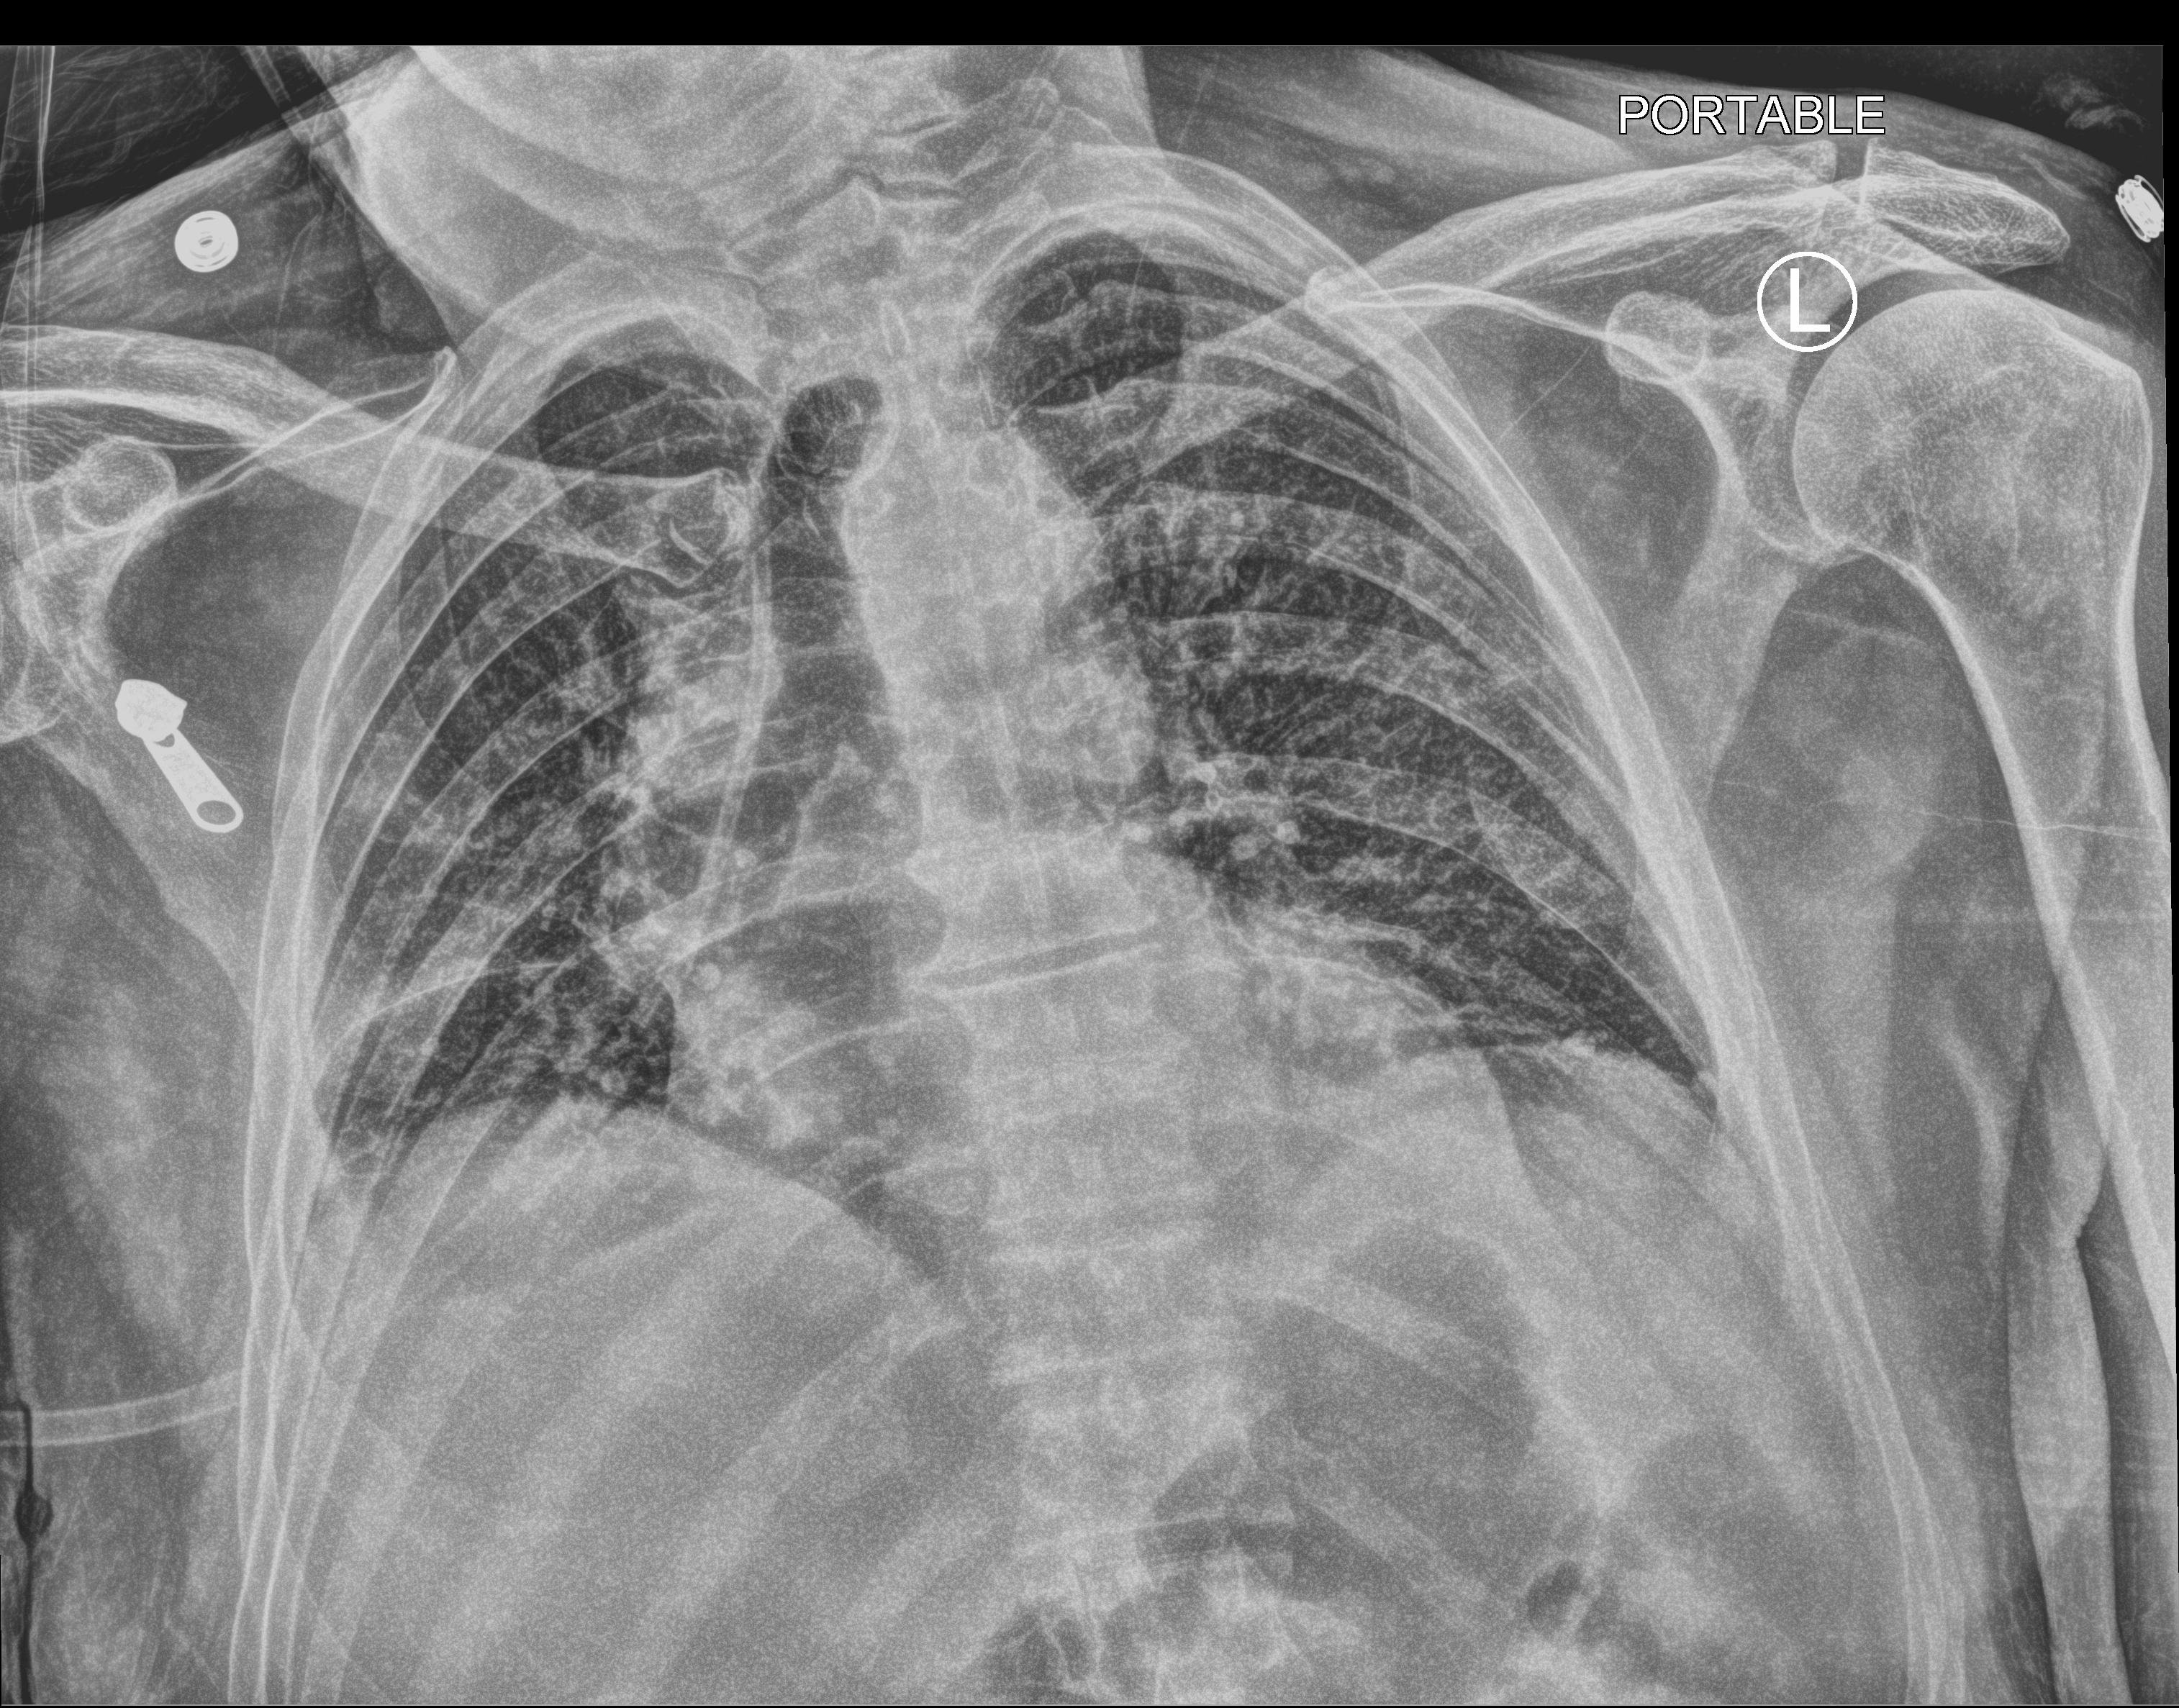
Chest X-ray (portable); anteroposterior (AP) projection. Male patient hospitalised with COVID-19, age 75–90 years.
From the hospital-stay record, not from the radiograph (when in the stay this image was taken is not recorded):
- smoking status (admission record): never